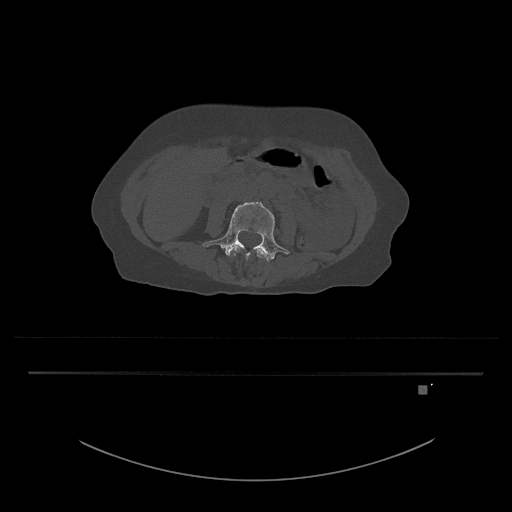
CT including the spine, one axial slice. Position 376 of 797 along the scan axis. Bone window (W 1800 / L 400 HU). 512 × 512 image matrix, field of view 500 × 500 mm. Patient: female, 57 years. Case-level facts recorded for this patient, not image findings: primary cancer: cervical.
Outlined on this slice (semi-automatically segmented with operator editing):
- L3 vertebra: bounding box (x1, y1, x2, y2) in pixels: (232, 249, 266, 259)
- L4 vertebra: (202, 201, 290, 262)